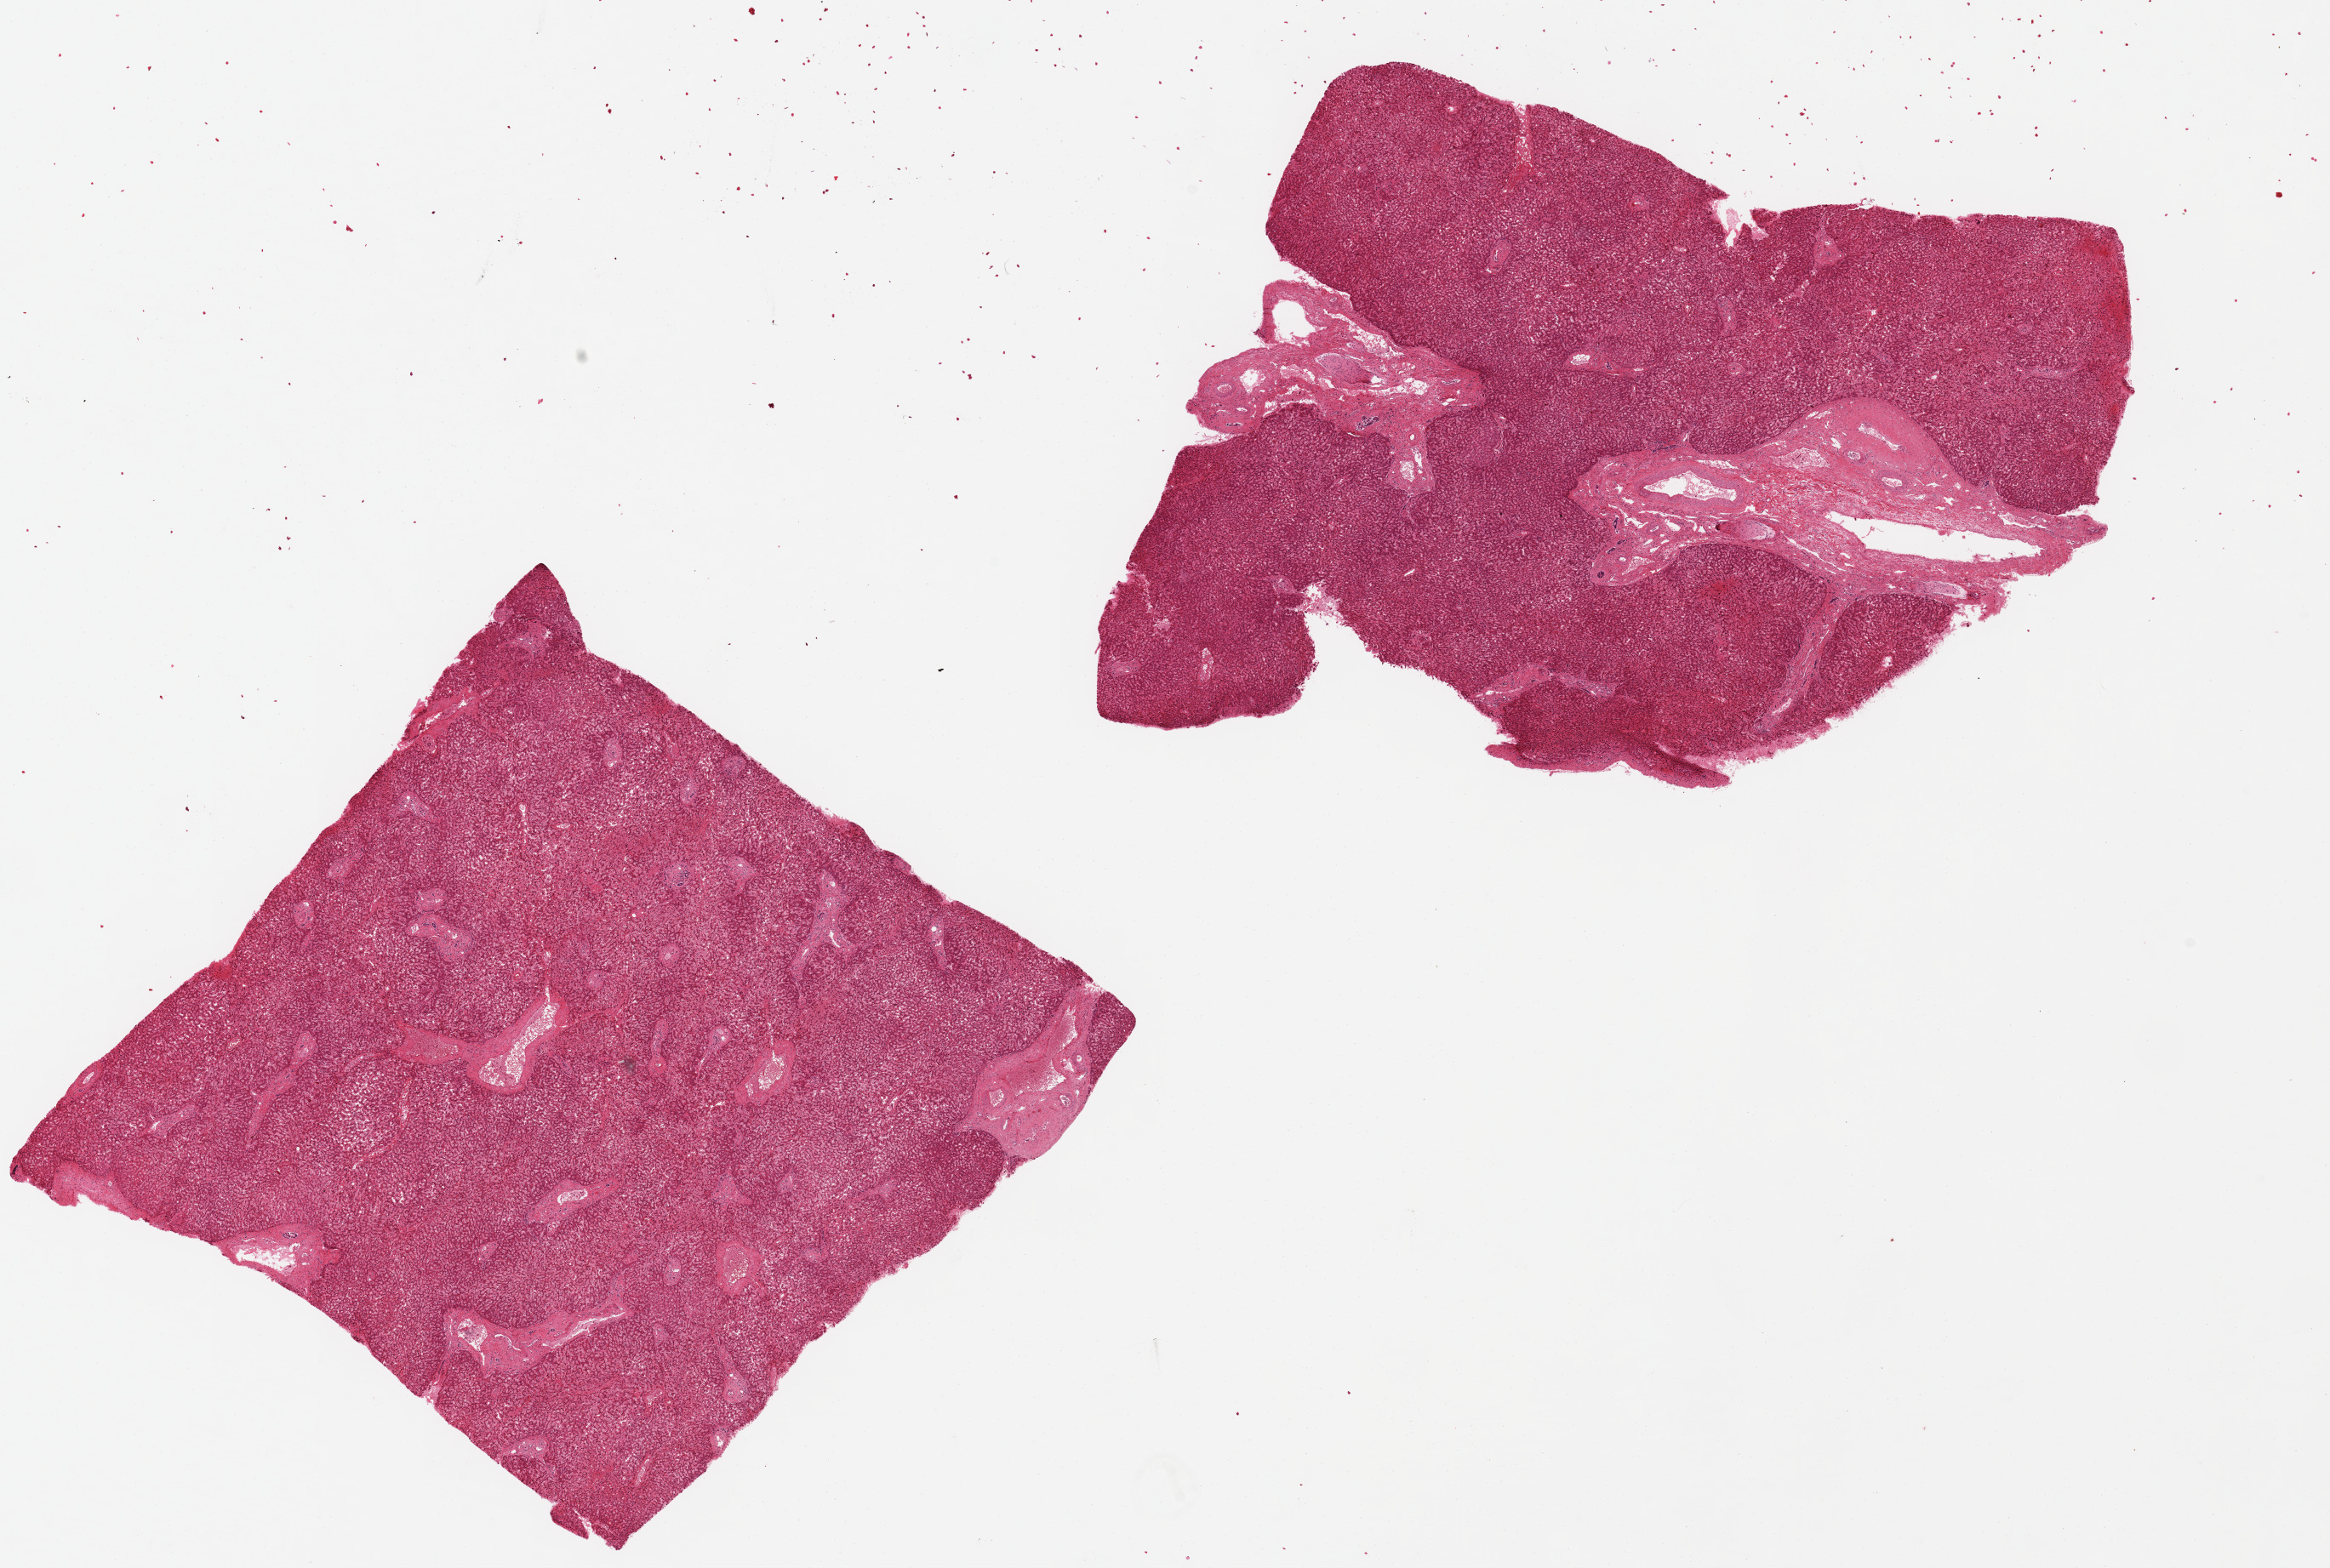
Hematoxylin and eosin (H&E) whole-slide image, whole scanned area (about 21.7 x 14.6 mm) shown as a low-resolution overview. PAXgene-fixed paraffin-embedded (PFPE) section. Section of liver (target tissue). Donor tissue sample. Donor sex: female.
Reviewer comment on this tissue sample: 2 pieces 8x7 & 7x7 mm; moderate sinusoidal congestion; fibrovascular area 4.7x1.8 mm at center of one piece.